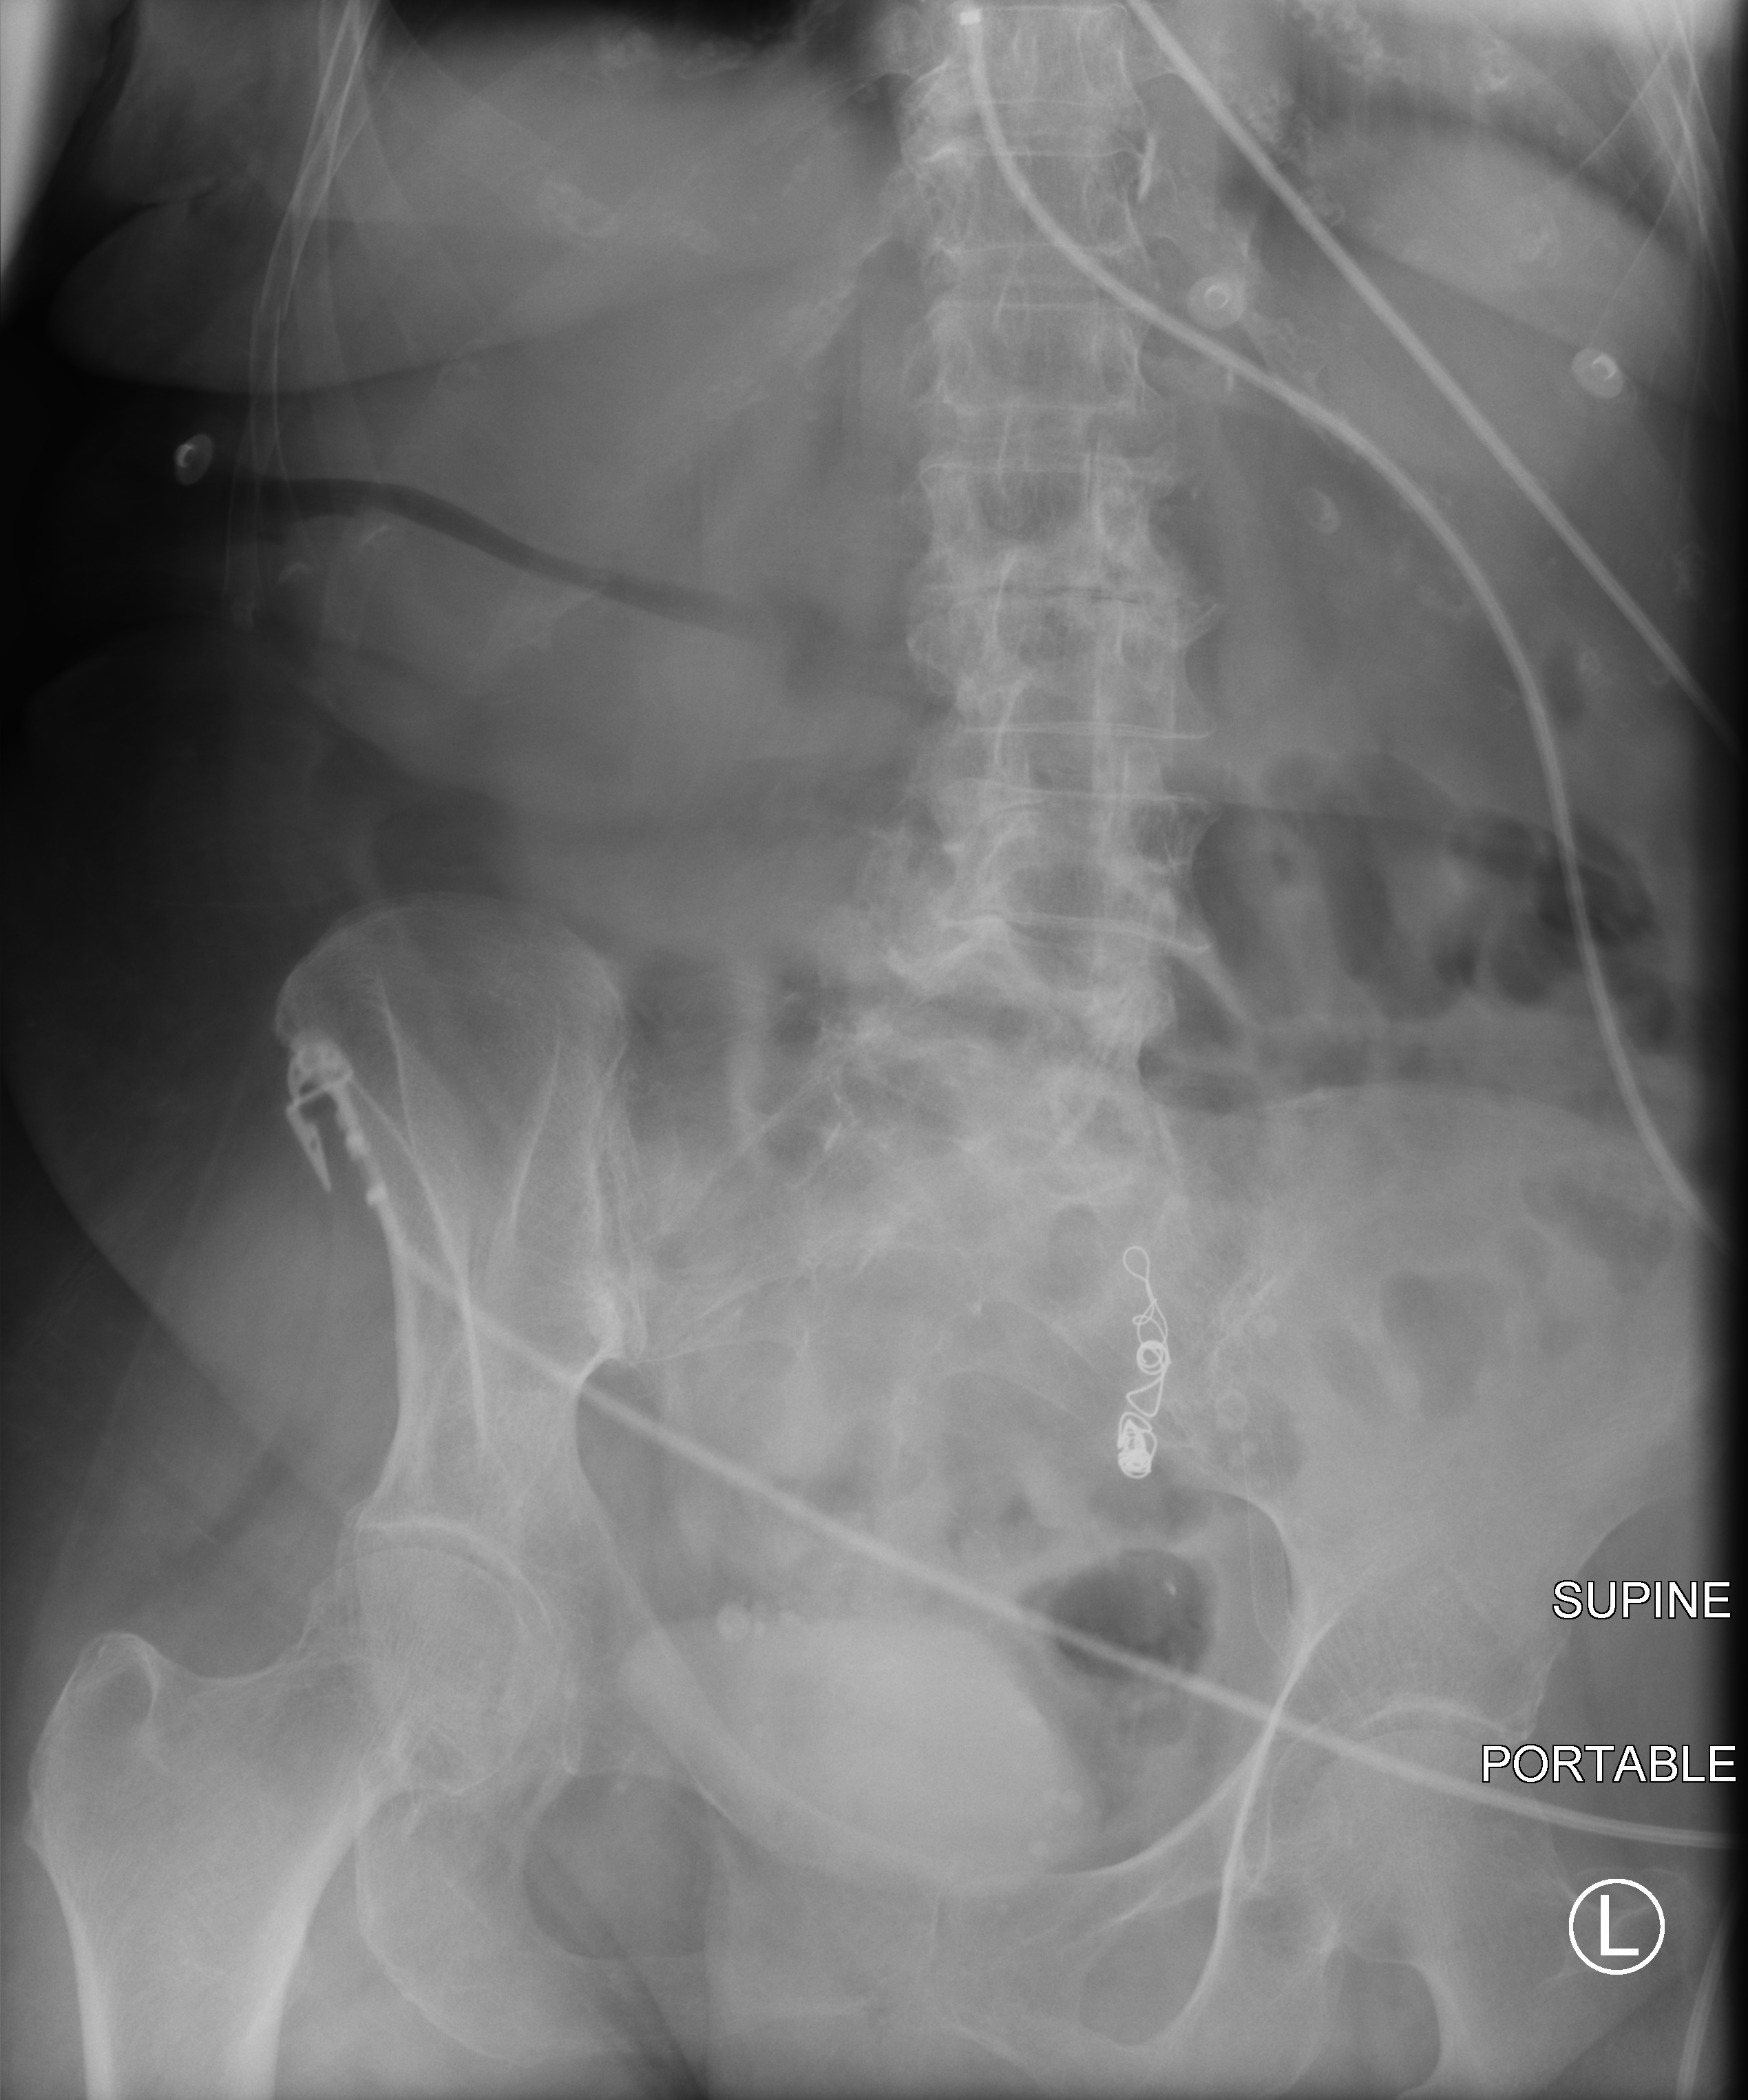
Abdomen X-ray (portable), anteroposterior (AP) projection. Patient hospitalised with COVID-19; female, aged 75–90 years.
Admission-level facts for this patient (not findings on this image; timing relative to this image not recorded): length of hospital stay: 6 days; mechanically ventilated during this hospital stay: no; admitted to intensive care during this hospital stay: no.